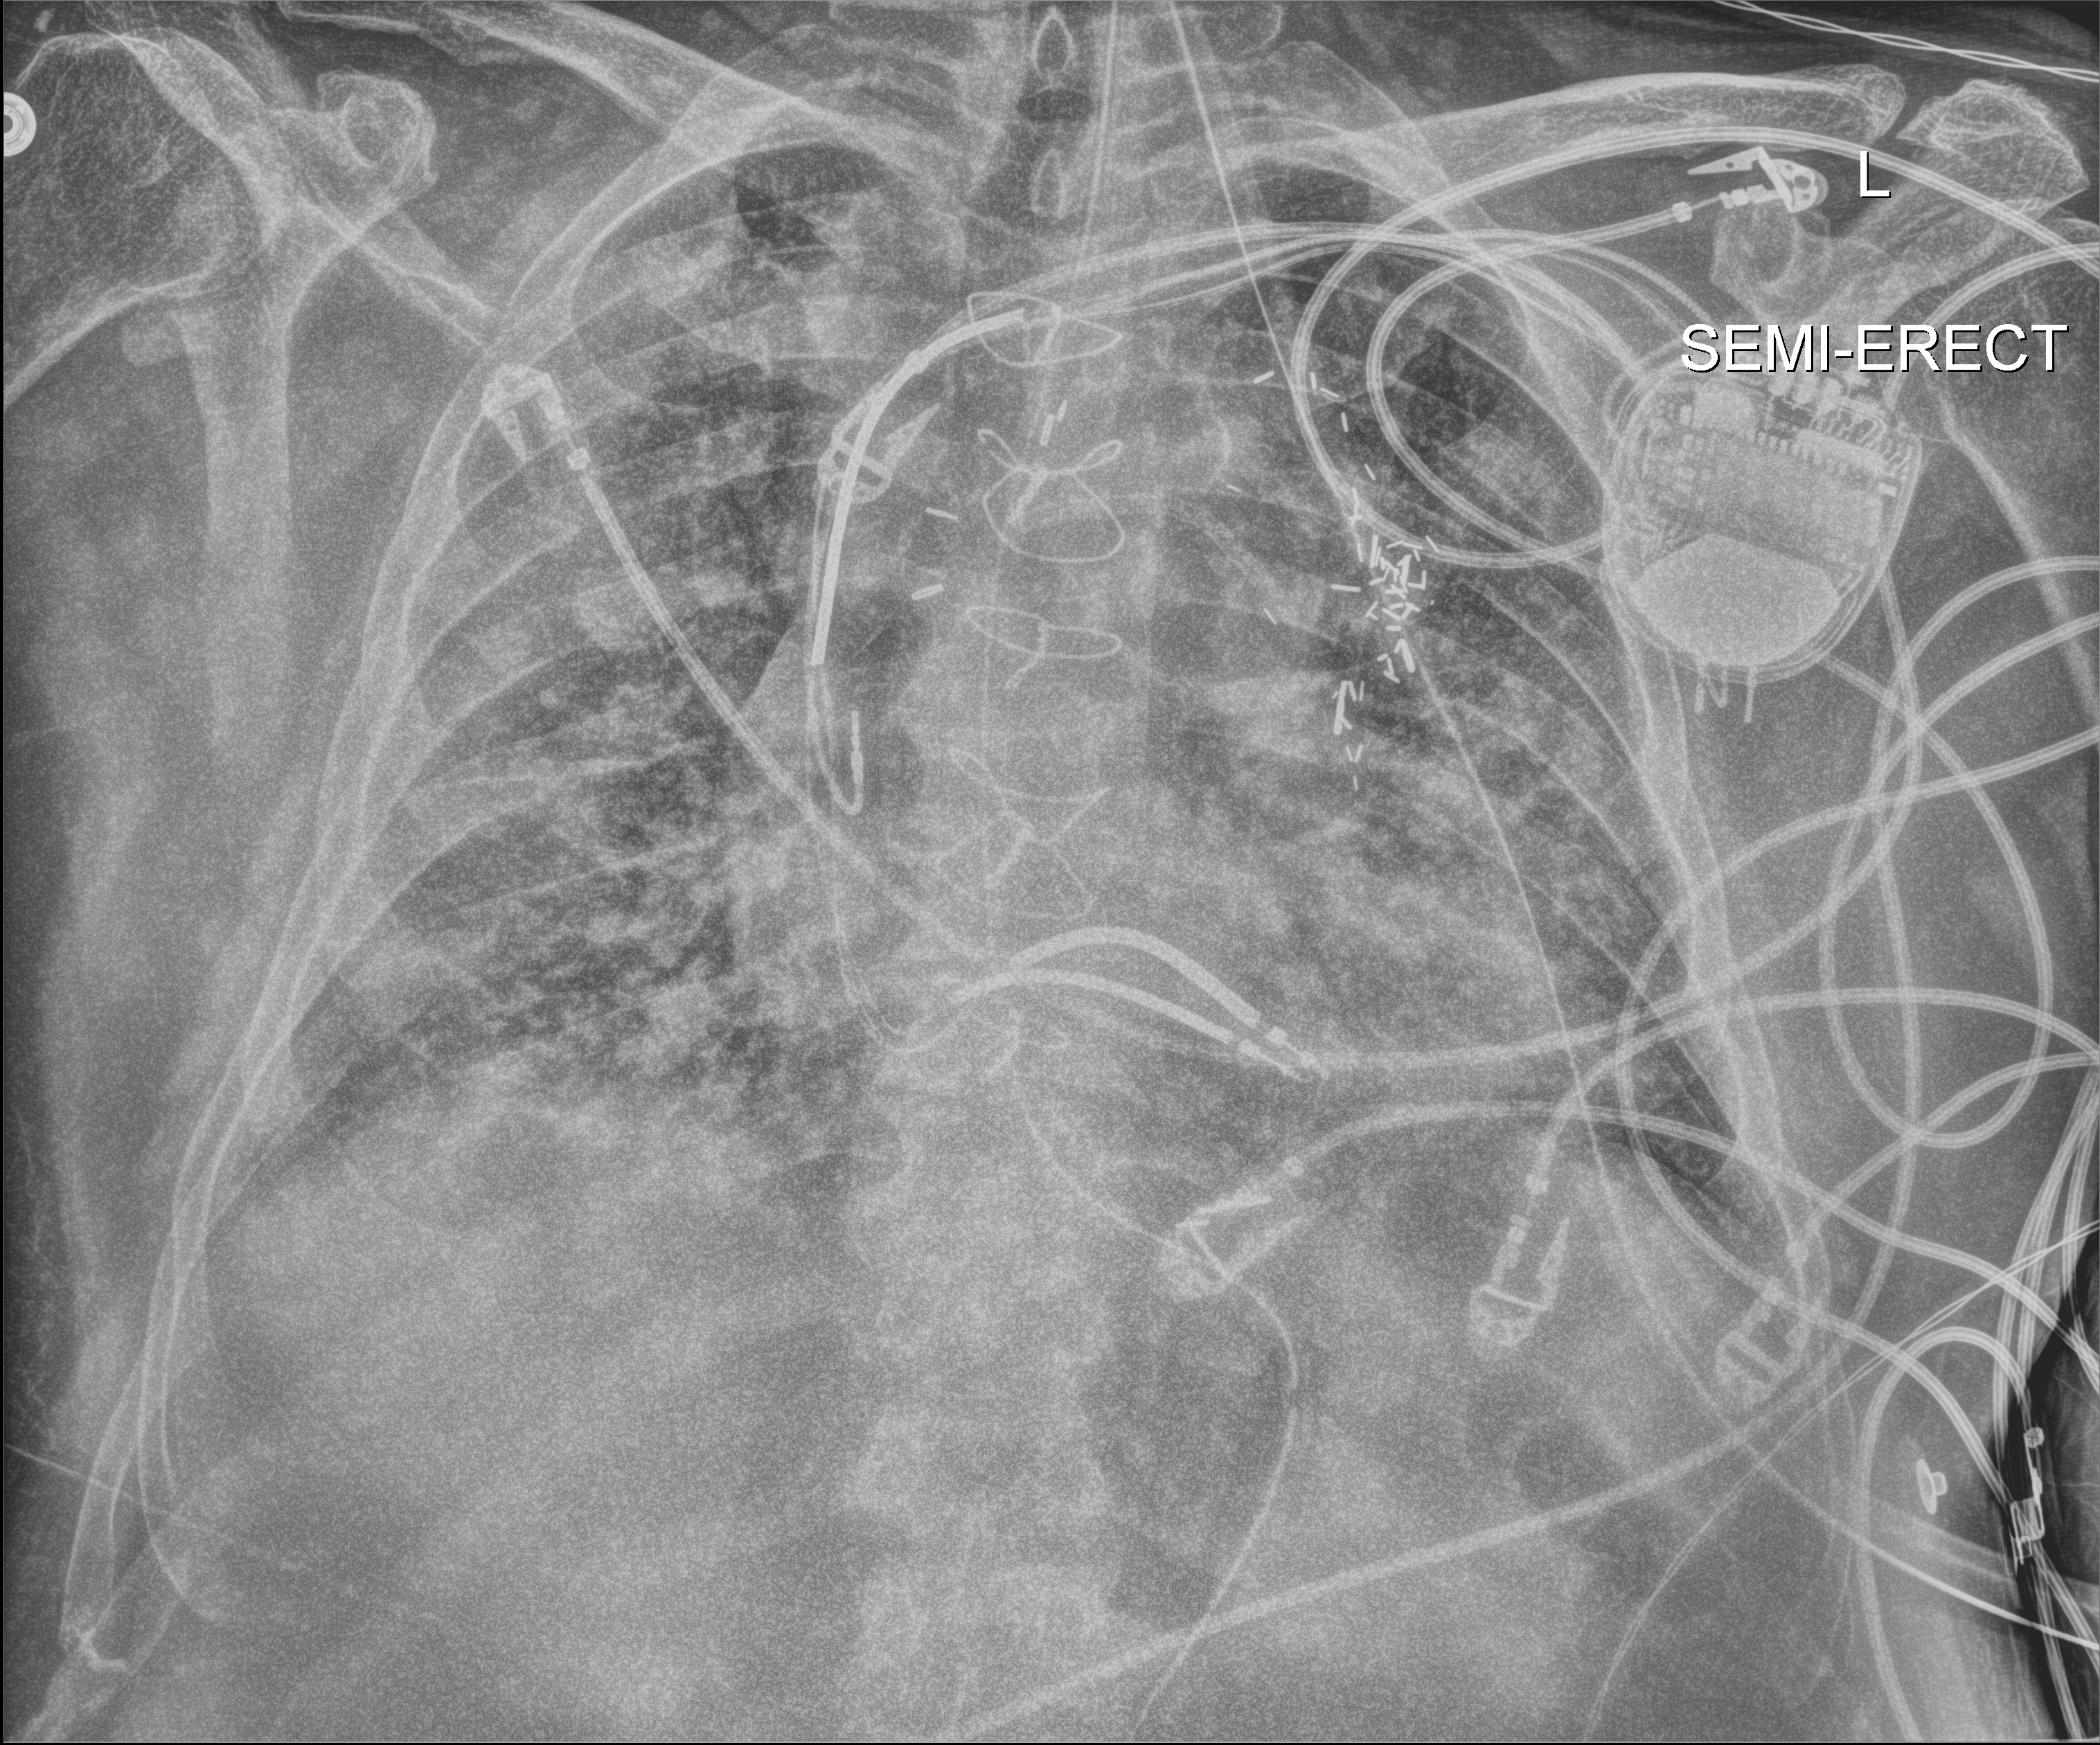
Chest X-ray (portable), anteroposterior (AP) projection. Male patient hospitalised with COVID-19, age 60–74 years.
From the hospital-stay record, not from the radiograph (when in the stay this image was taken is not recorded): mechanically ventilated during this hospital stay: yes.